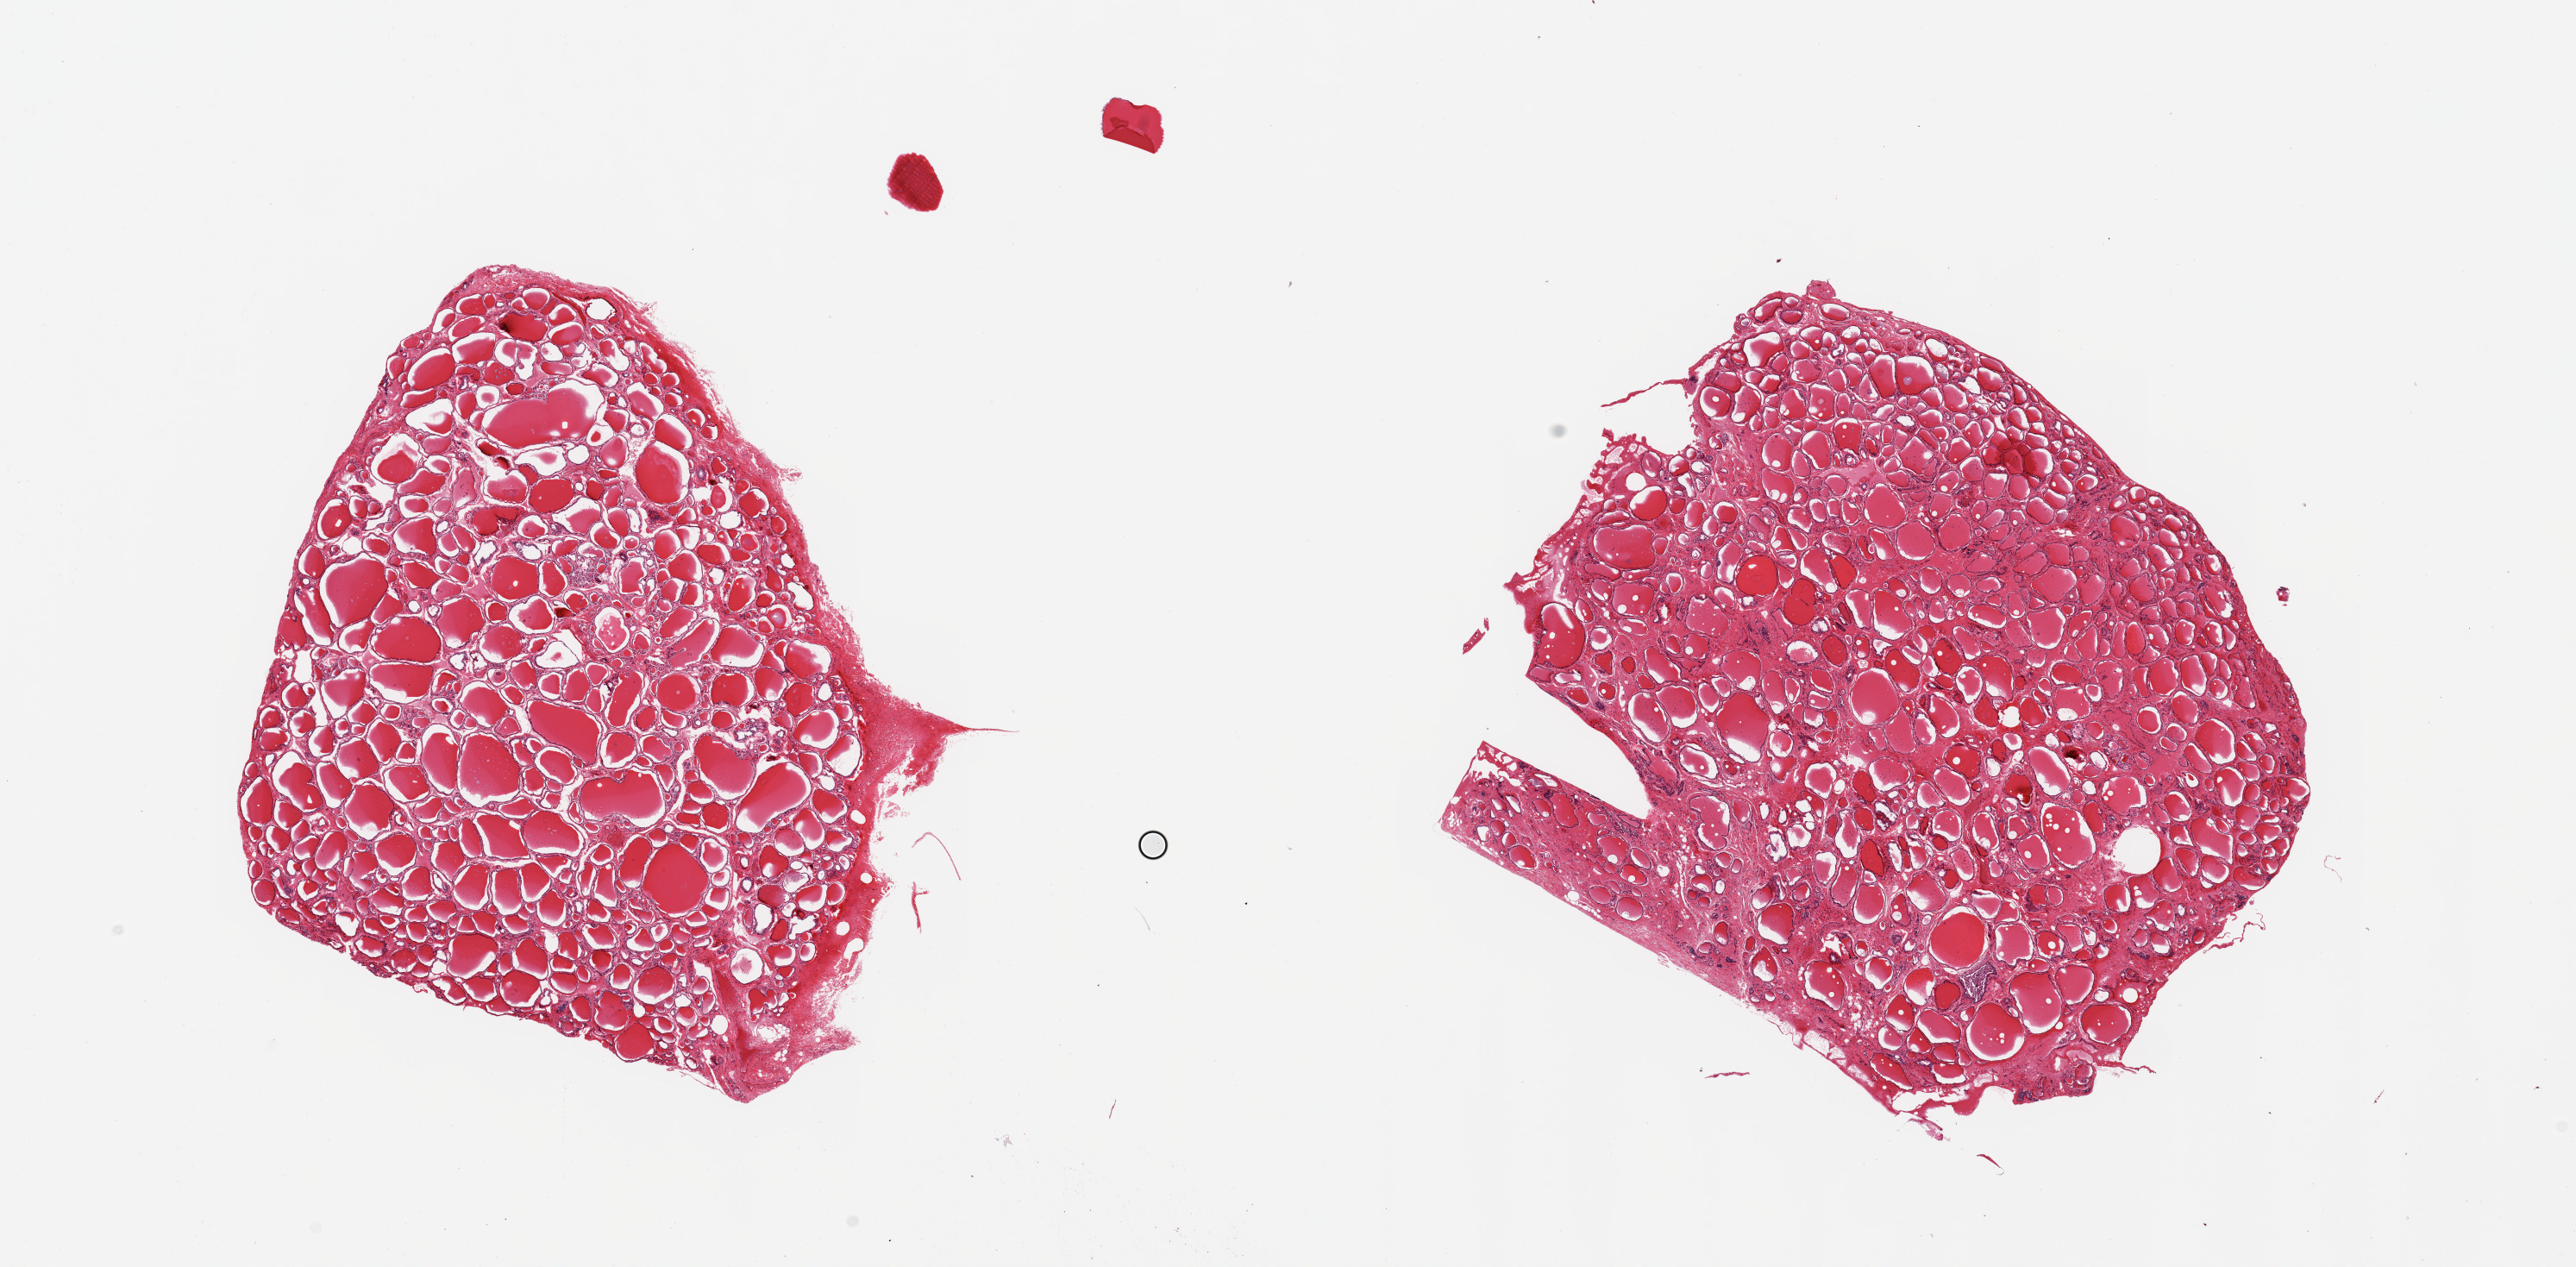
Whole-slide image, hematoxylin and eosin (H&E) stain, brightfield, whole scanned area (about 23.6 x 11.6 mm) shown as a low-resolution overview. PAXgene-fixed, paraffin-embedded tissue. Sampled site (target tissue): thyroid. Donor tissue sample.
Pathologist's review note for this sample: 2 pieces, no significant abnormalities.